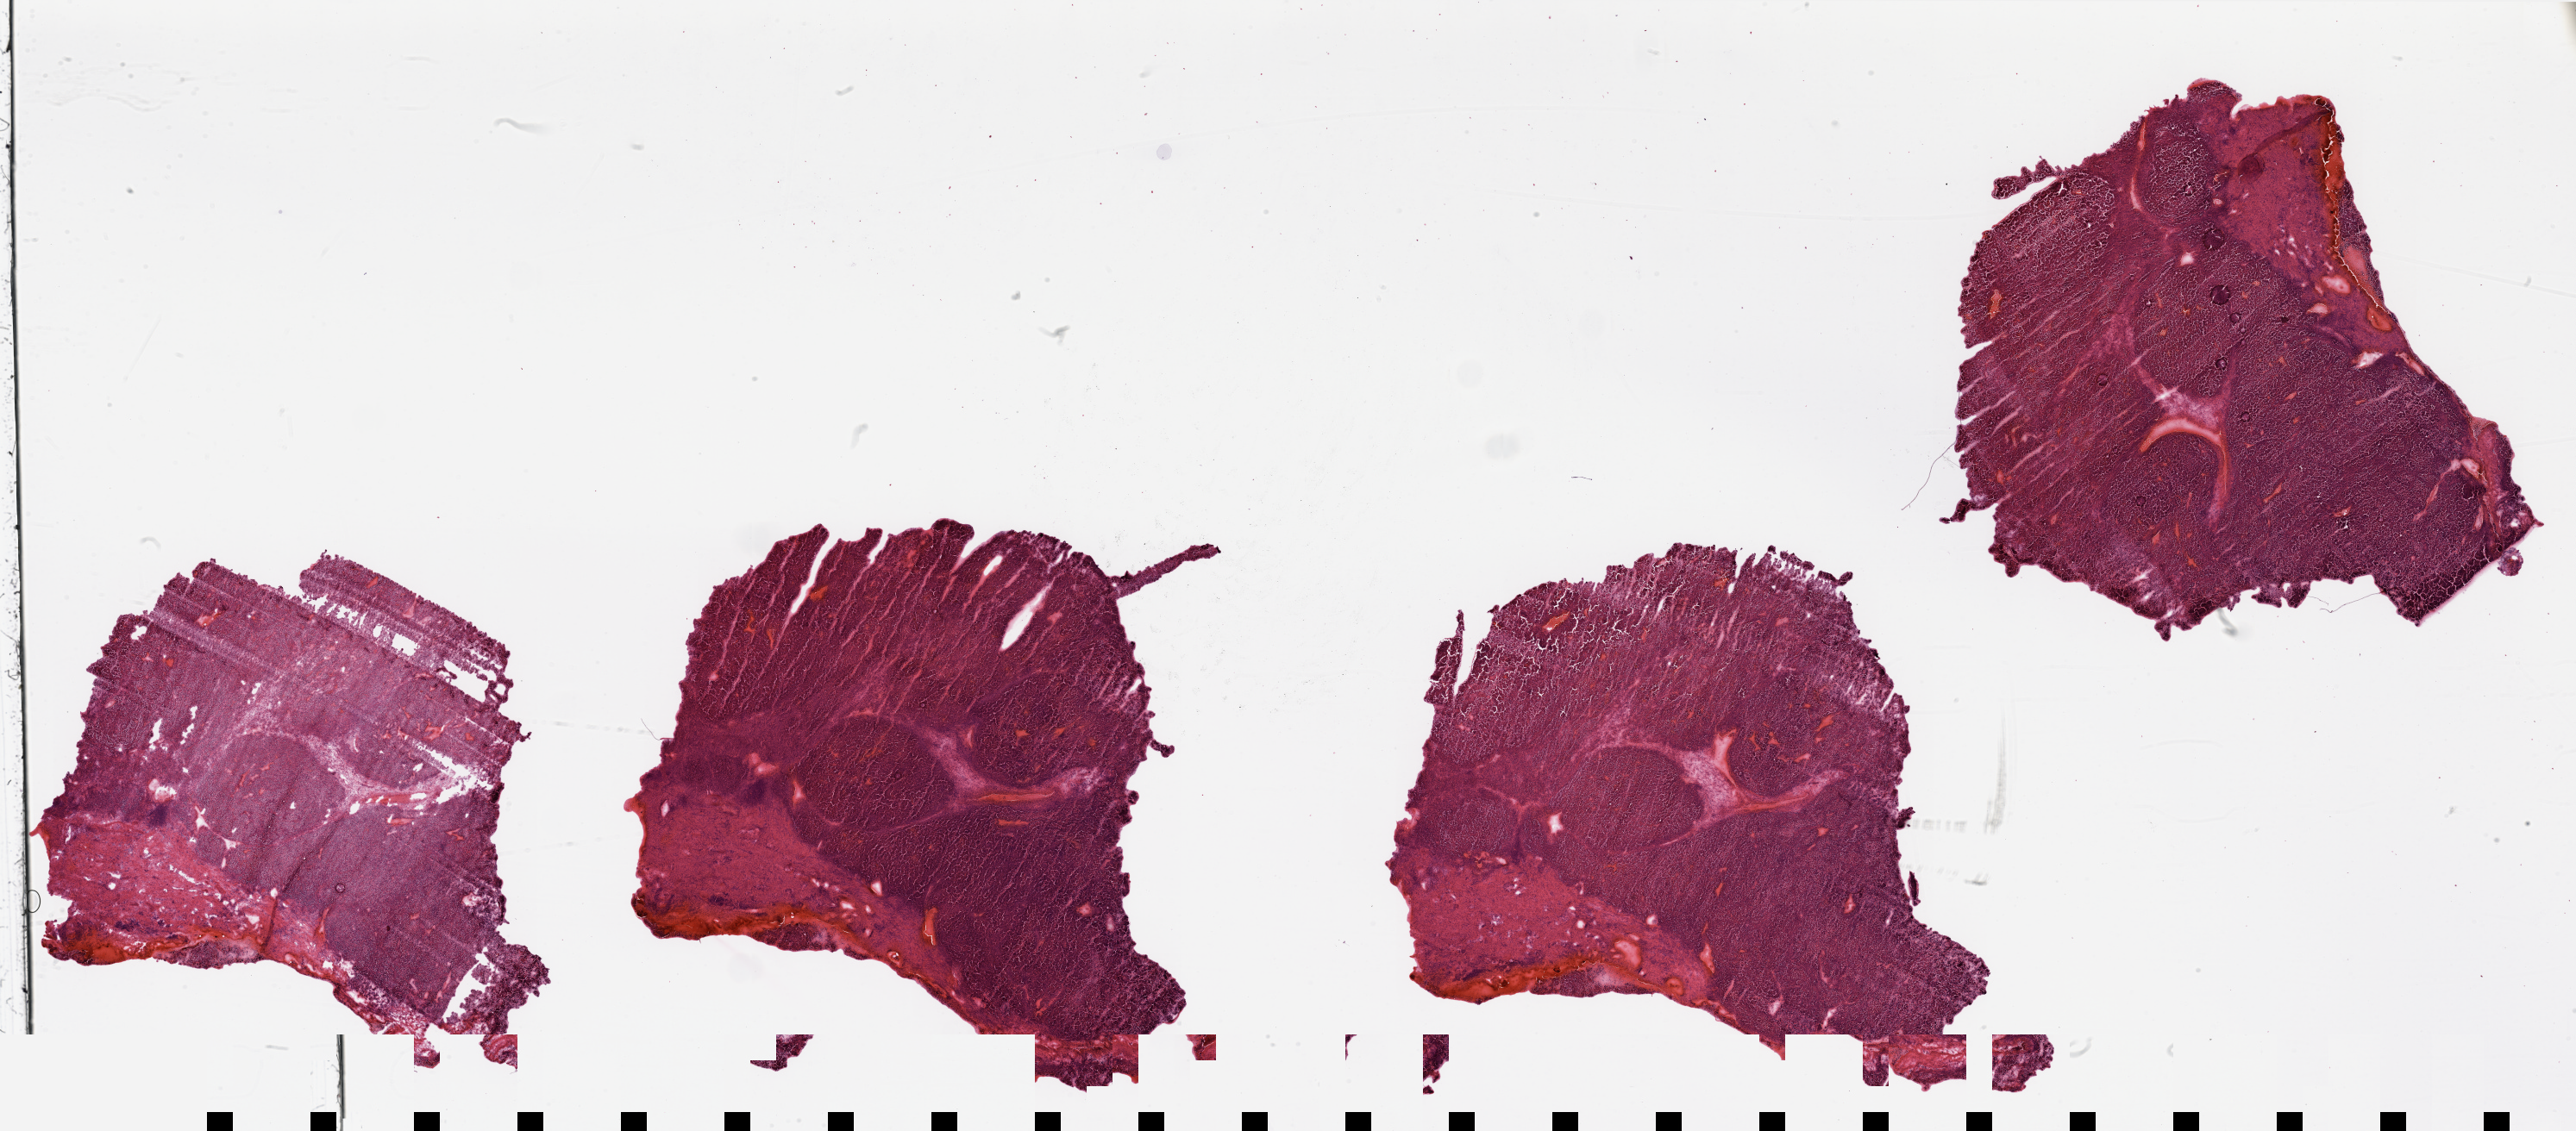
Hematoxylin and eosin (H&E) stained whole-slide image, shown as a low-resolution overview of the whole scanned area (about 47.3 x 20.8 mm, slide scanned at 20x), tumour tissue sample, sampled site: kidney. Male, 68 y/o. Histologic grade: G3 (poorly differentiated). Slide review estimates, as recorded: tumour nuclei 80%, necrosis 5%.
AJCC pathologic stage: III. Histologic diagnosis: Renal cell carcinoma, NOS. Primary tumour site (as recorded): lower pole.